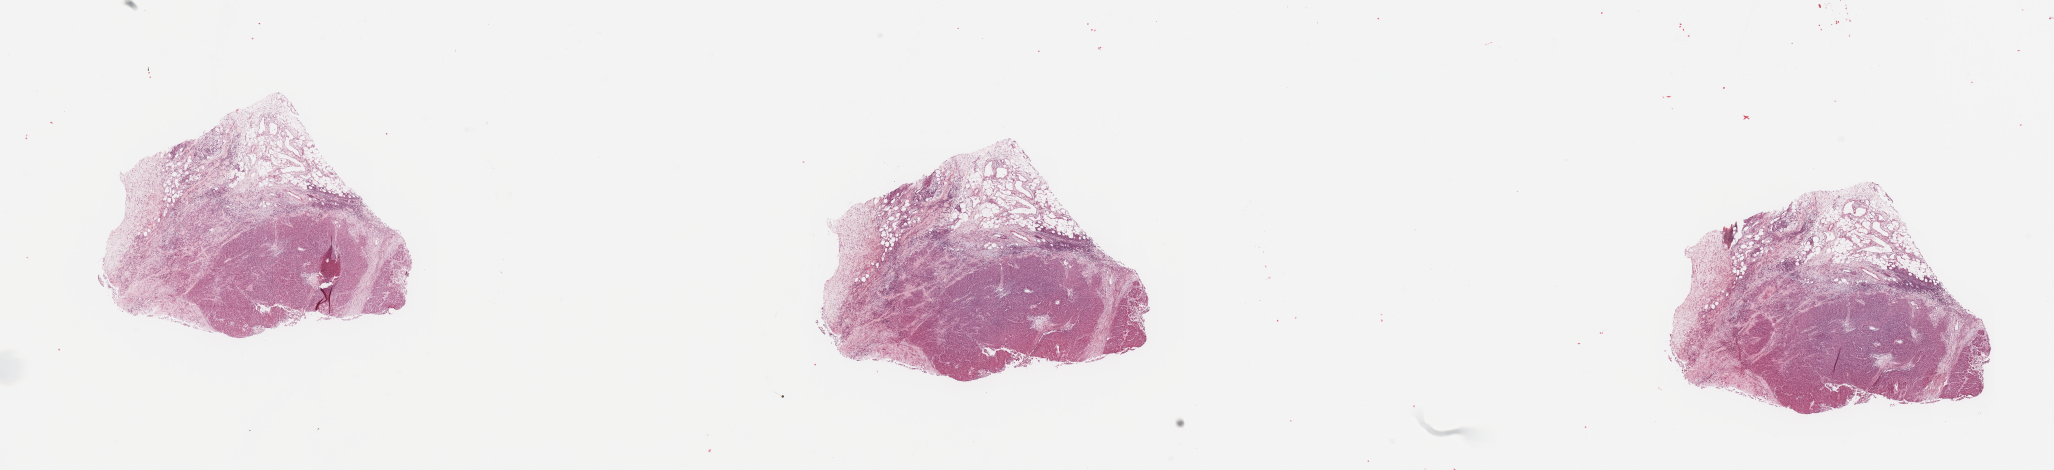
Digitized H&E tissue section (whole slide), shown as a low-resolution overview of the whole scanned area (about 32.5 x 7.4 mm, from a 20x scan); tumour tissue sample, sampled site: lymph node. Male, 64 y/o.
This section: metastatic tumour tissue. Patient diagnosis: Malignant melanoma, NOS.